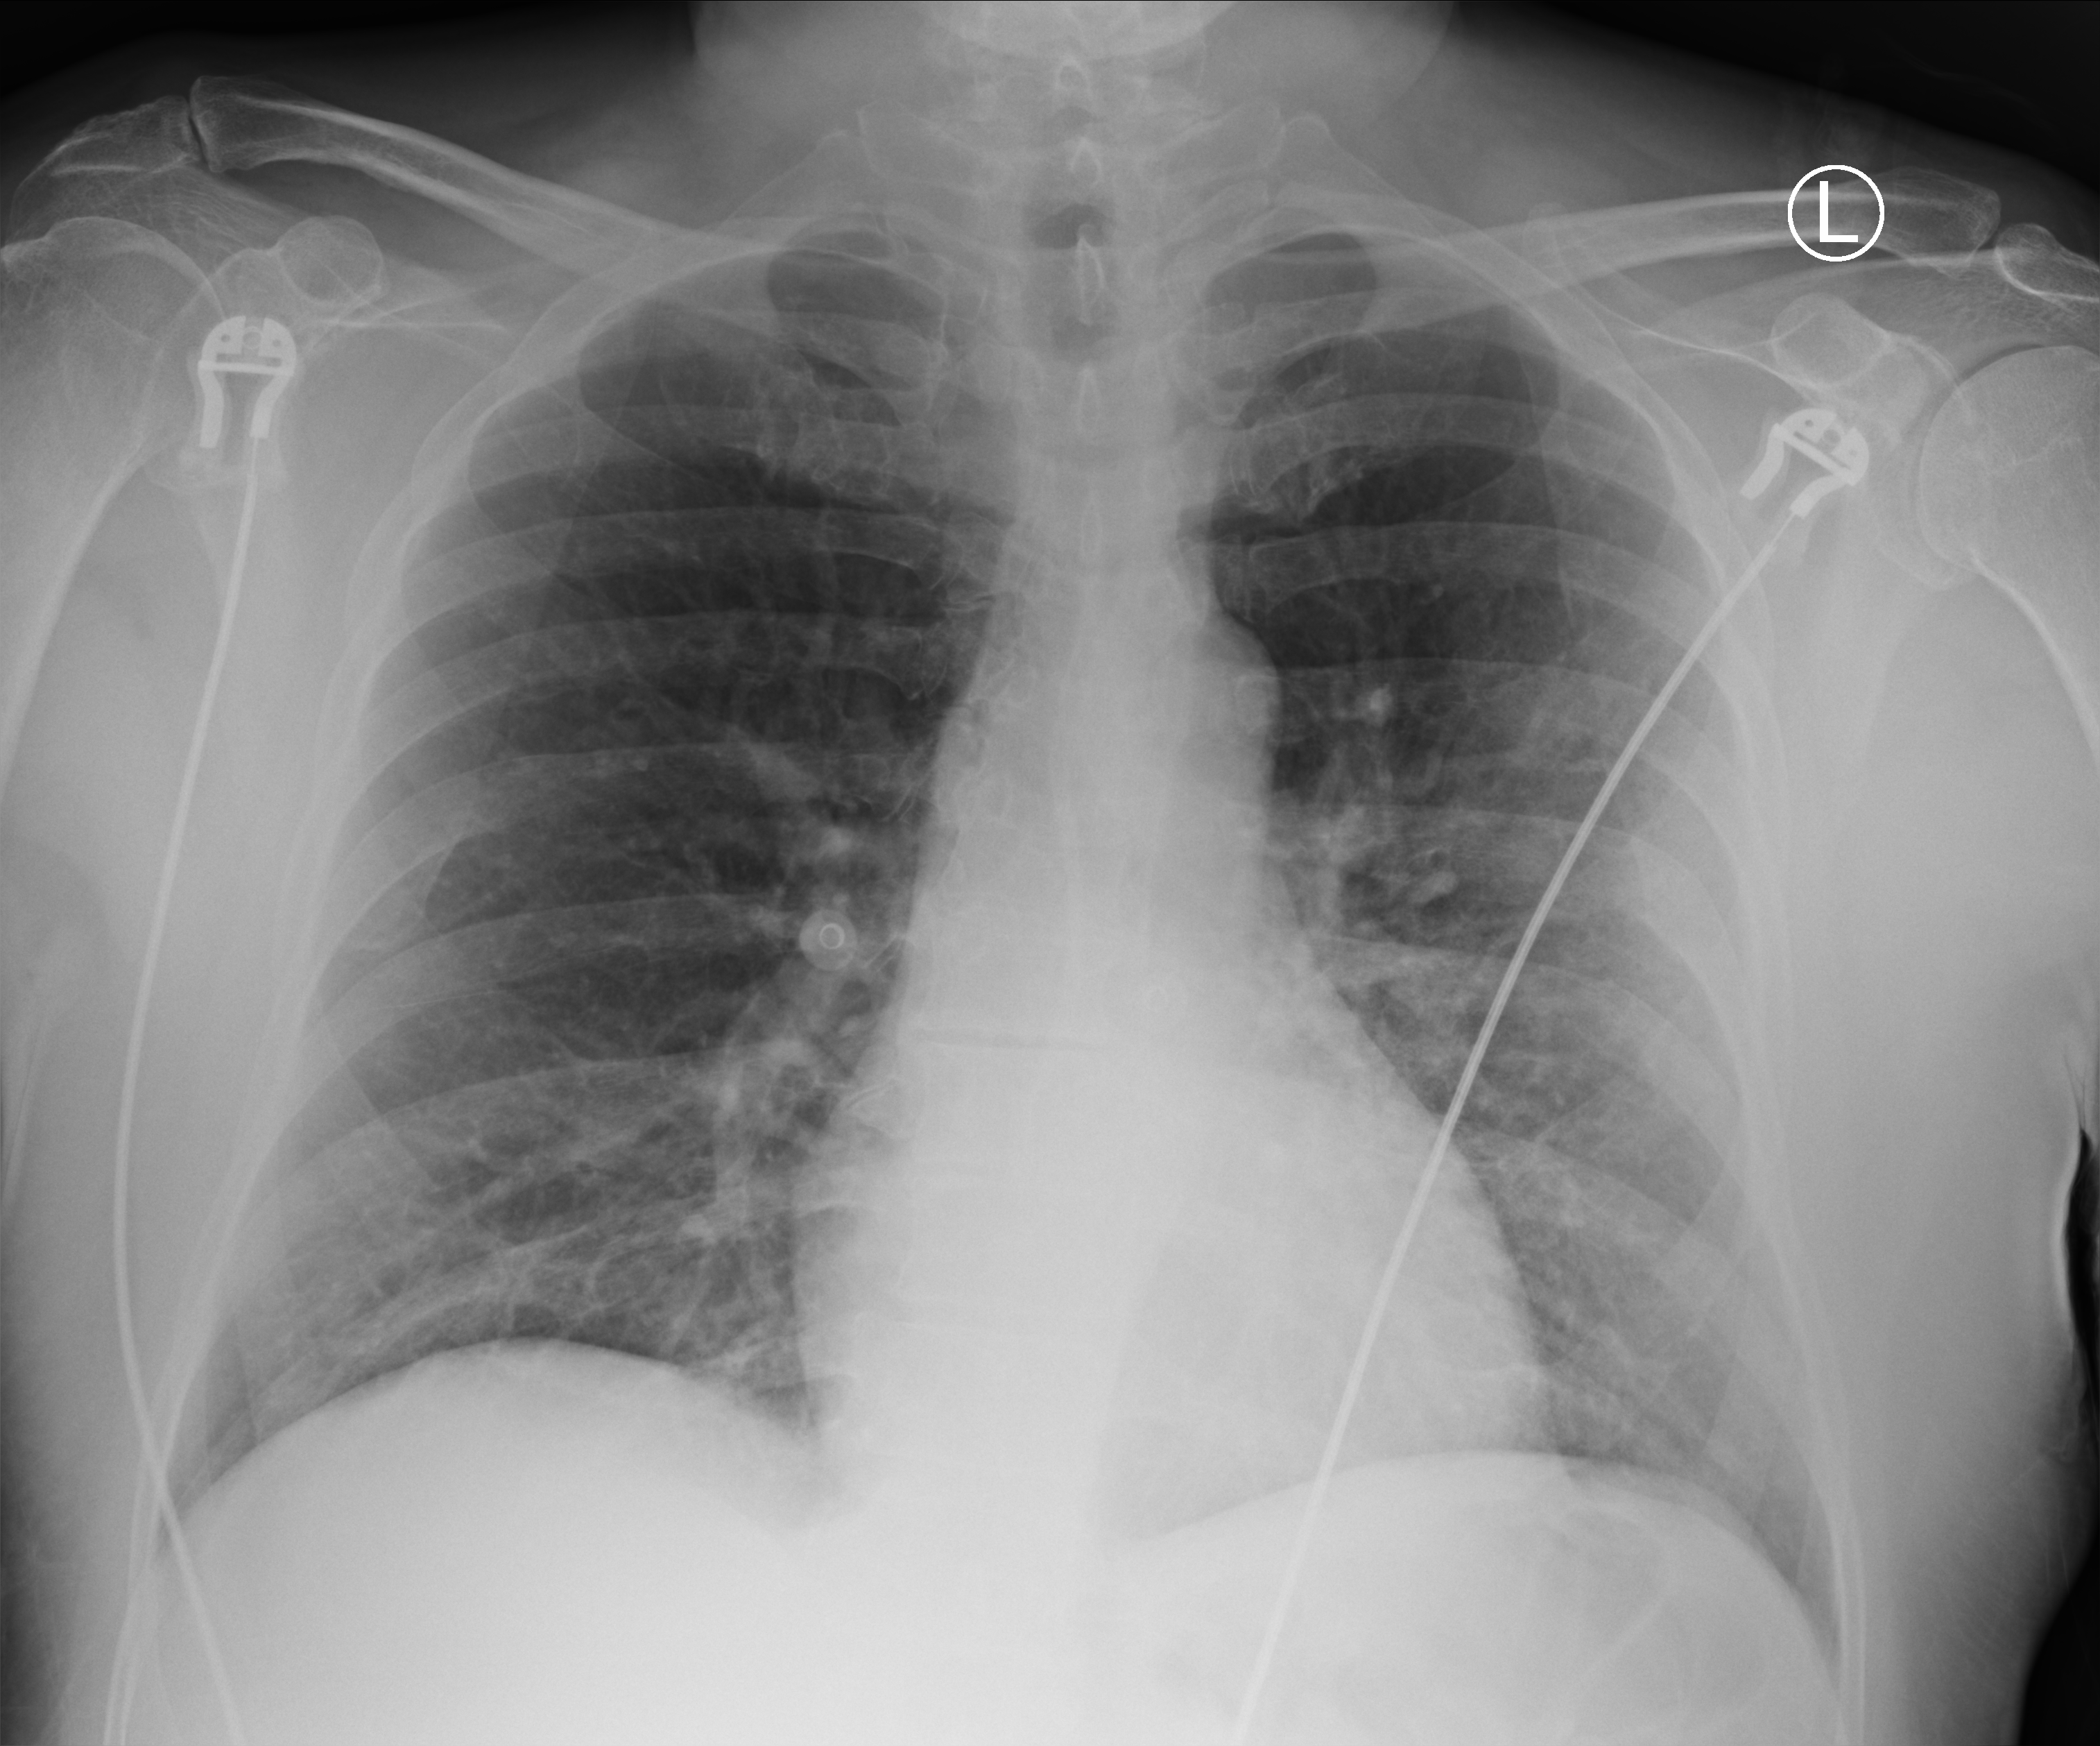
Bedside chest radiograph (computed radiography); anteroposterior (AP) projection. Male patient hospitalised with COVID-19, age 60–74 years.
From the hospital-stay record, not from the radiograph (when in the stay this image was taken is not recorded): length of hospital stay: 6 days; other chronic lung disease (admission record): no.